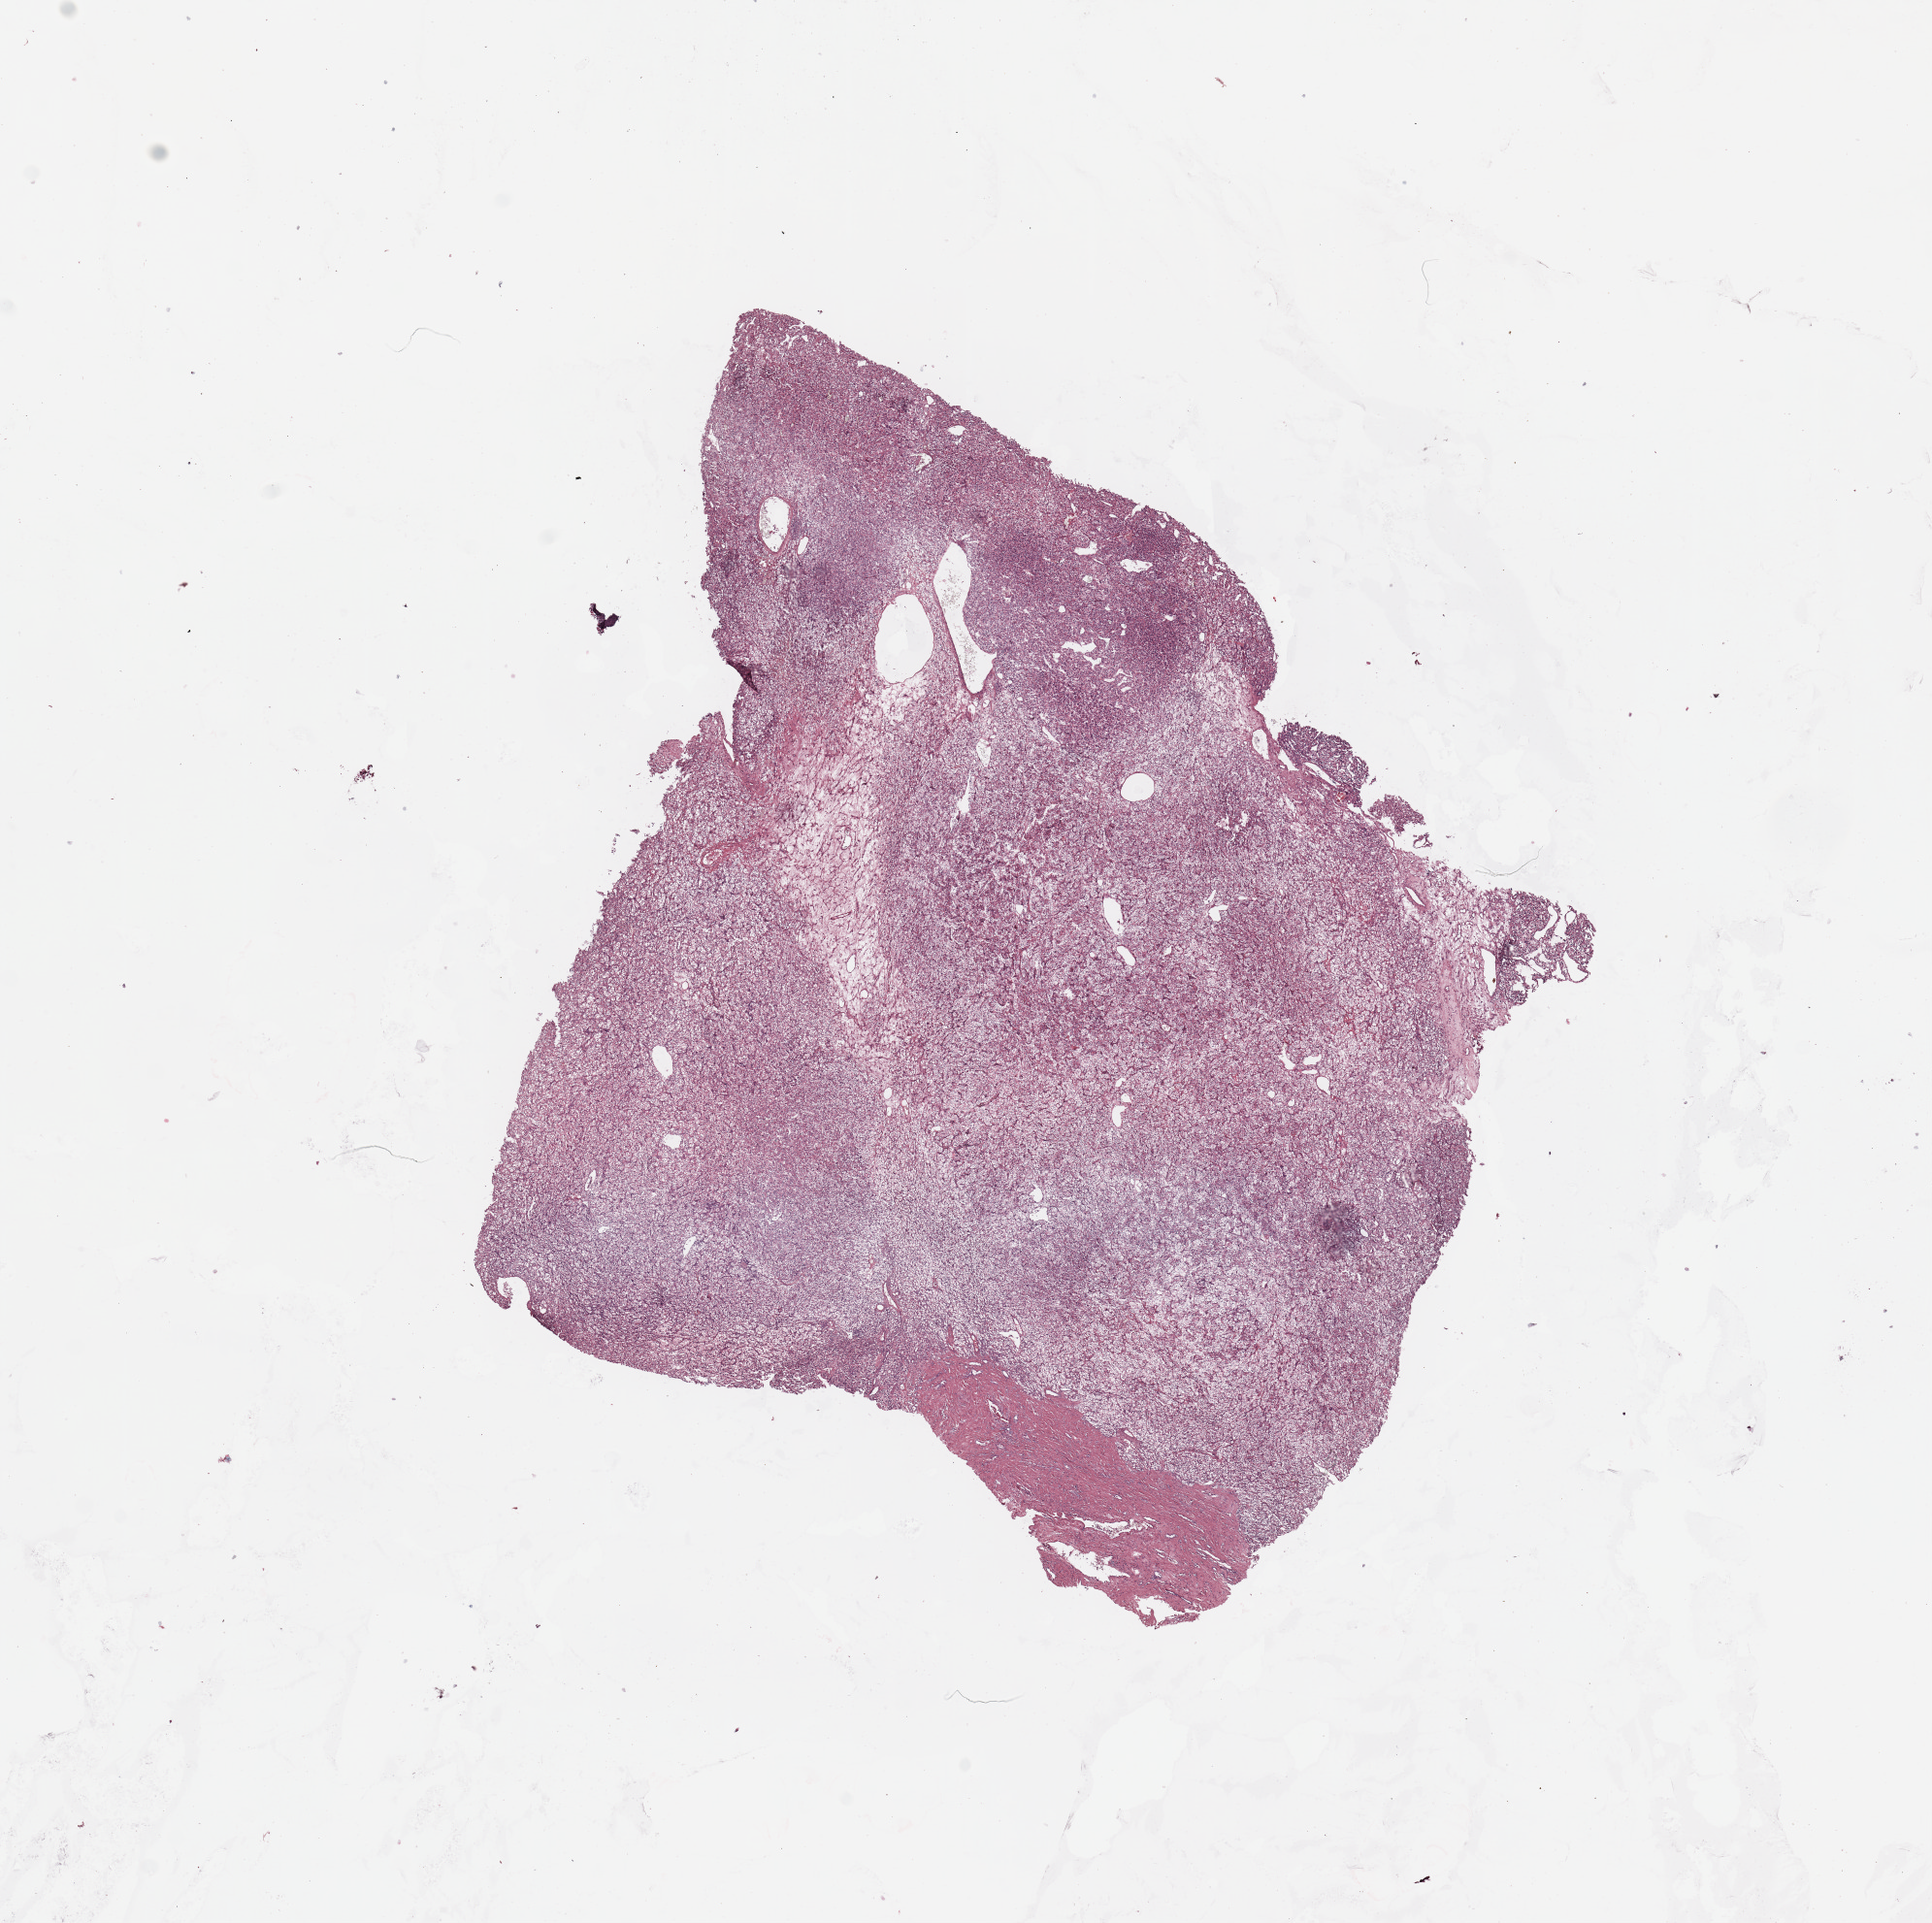
H&E-stained whole-slide image, shown as a low-resolution overview of the whole scanned area (about 15.8 x 15.7 mm). Tumour tissue sample, sampled site: kidney. Male, 80 y/o. Histologic grade: G2 (moderately differentiated). Composition of this section per pathologist review: tumour nuclei 95%, necrosis 5%.
Primary tumour site (as recorded): upper pole. Histologic diagnosis: Renal cell carcinoma, NOS. AJCC pathologic stage: I.